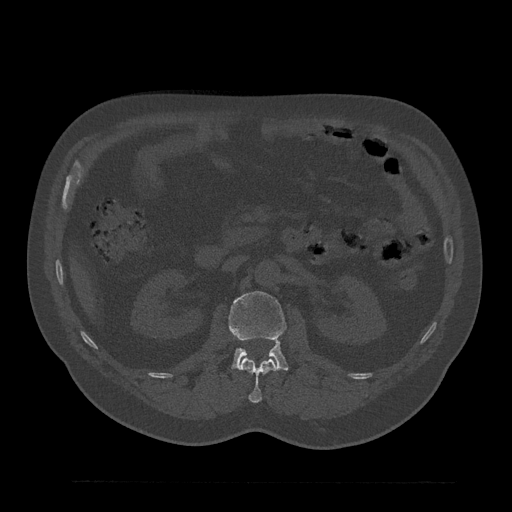
CT including the spine, one axial slice; reconstruction kernel Br40s/3; 120 kVp; bone window (W 1800 / L 400 HU); 0.5 mm slice thickness; 512 × 512 image matrix. Male patient, age 61 years. Case-level facts recorded for this patient, not image findings: primary cancer: prostate.
Annotated regions visible in this slice (semi-automatic segmentation, software-assisted and operator-edited):
- L1 vertebra: bounding box (x1, y1, x2, y2) in pixels: (239, 358, 279, 403)
- L2 vertebra: (228, 291, 288, 370)